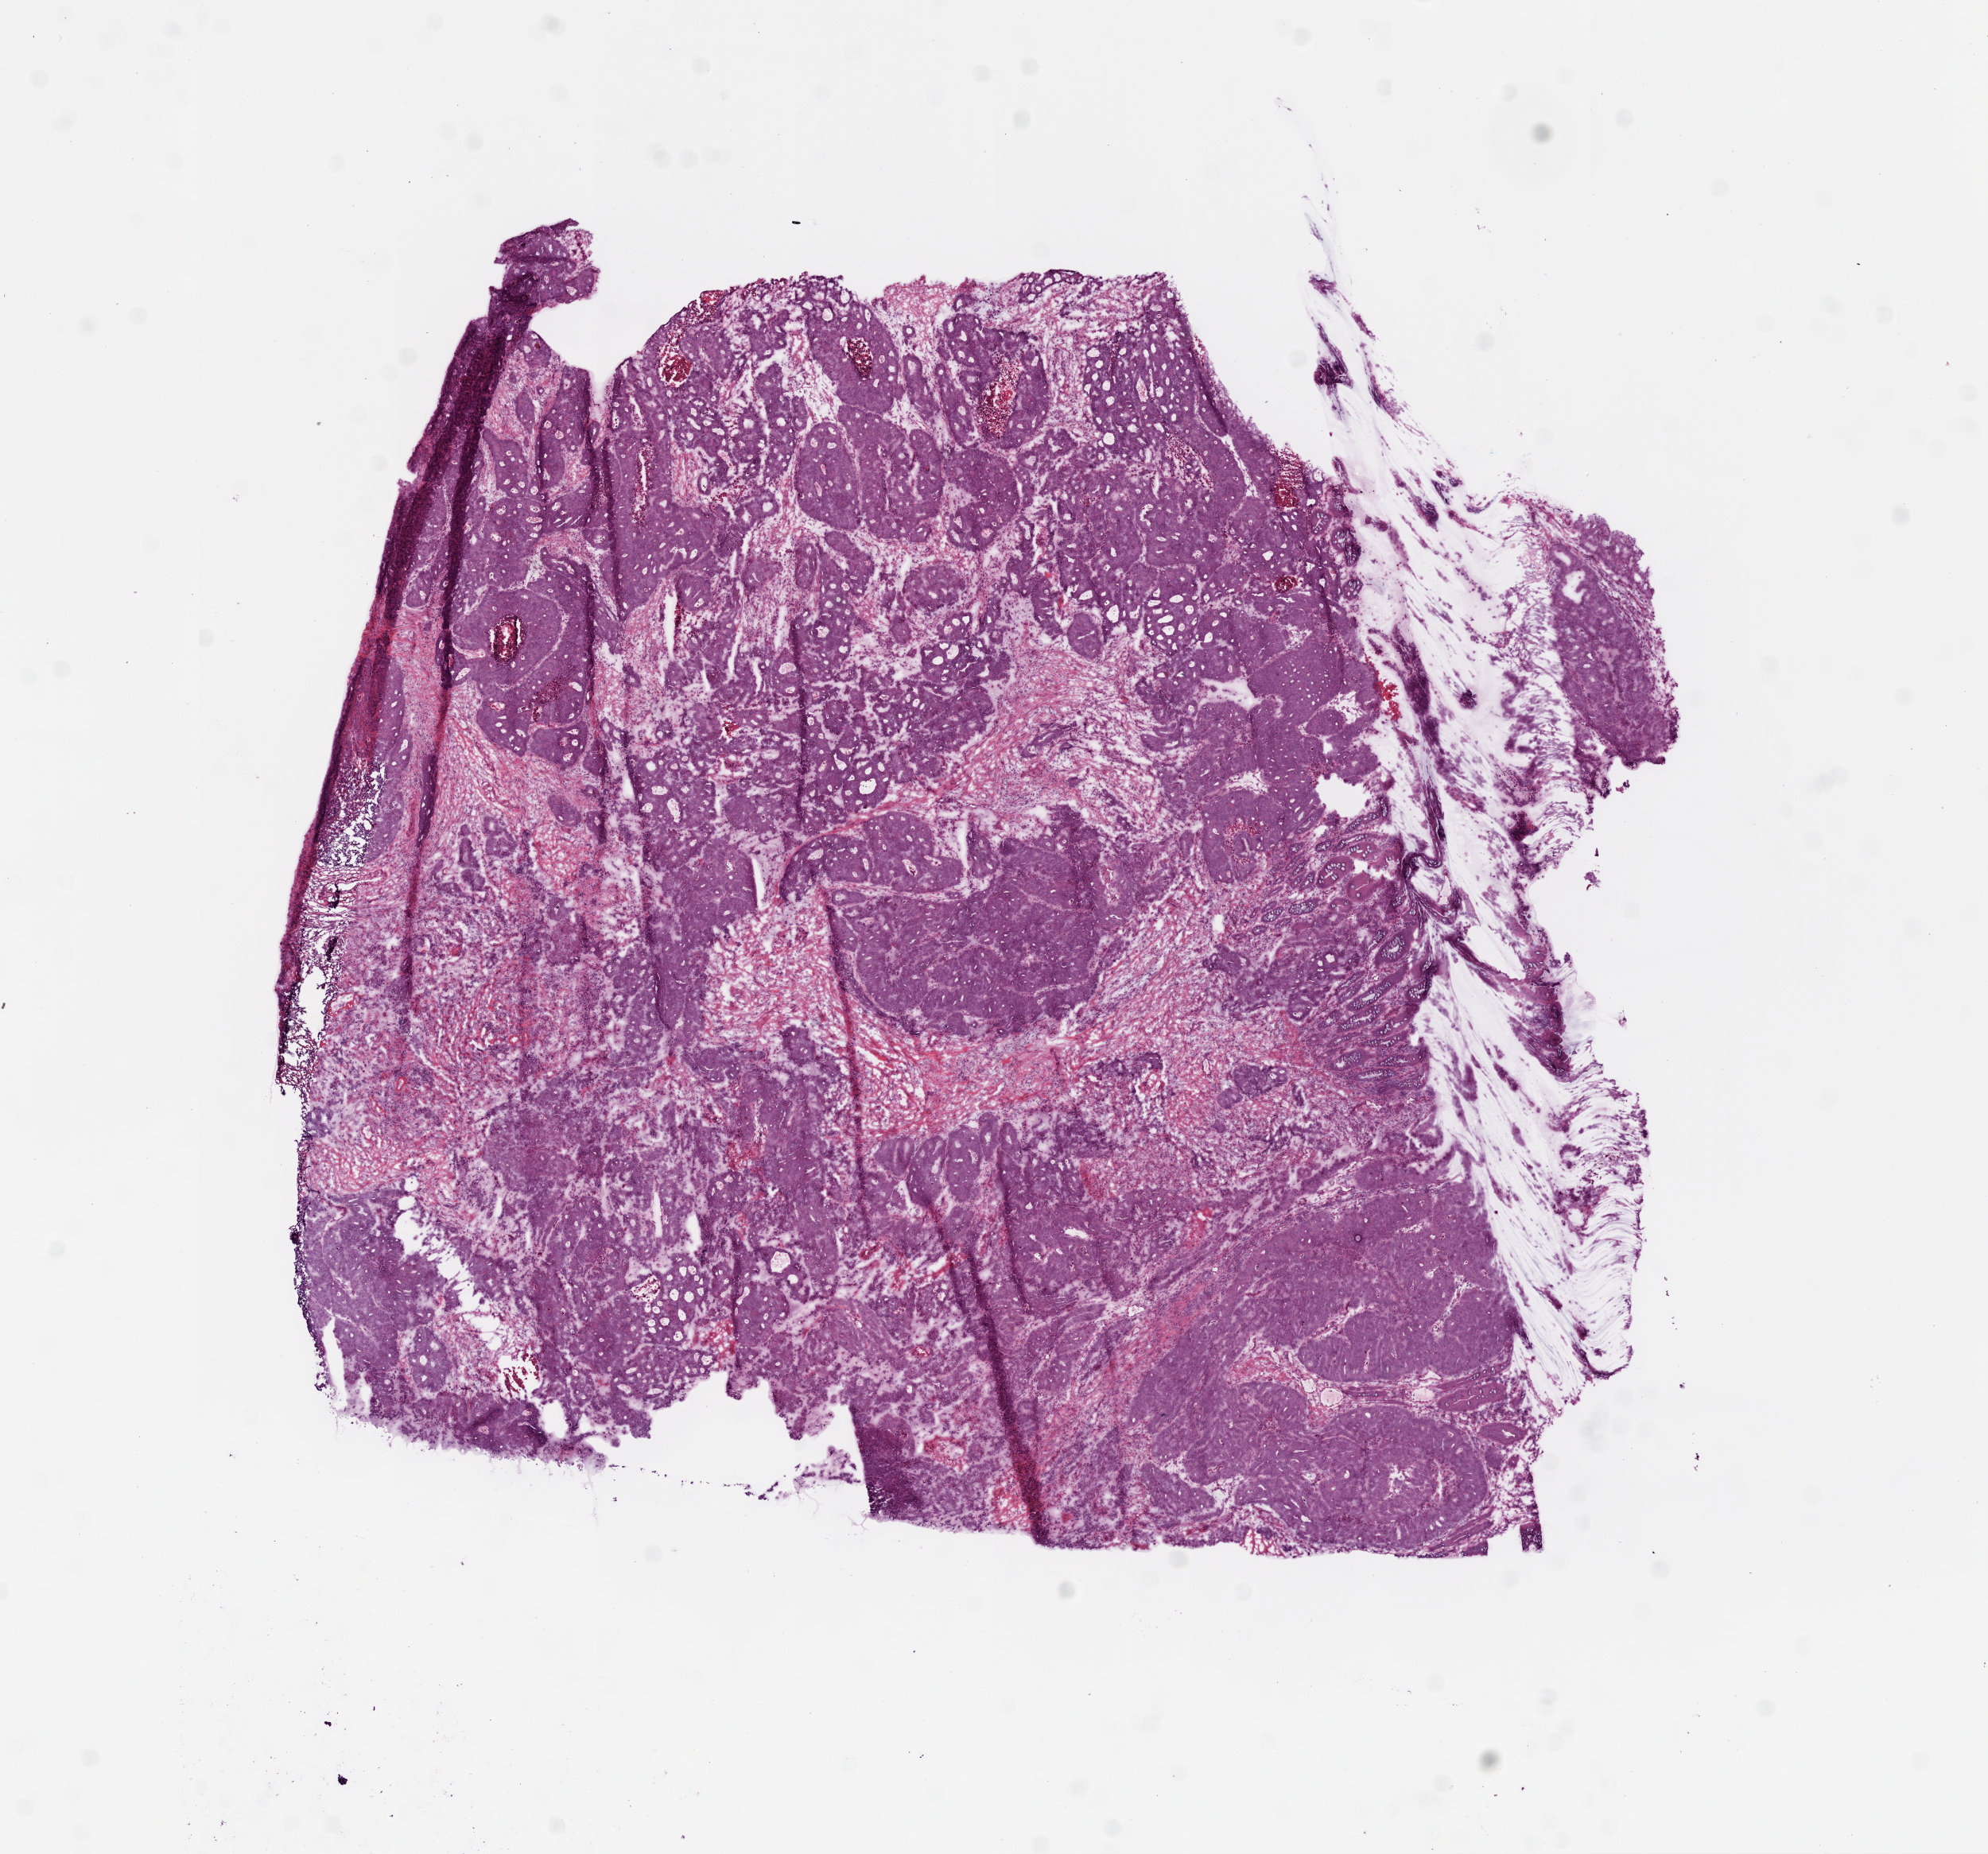
Whole-slide histology image, H&E — low-resolution overview of the scanned area, about 10.0 x 9.4 mm (from a 20x scan). Frozen section. Colon, primary tumour sample. Patient: male, age at initial diagnosis 59 years. Slide review estimates, as recorded: tumour cells 67%, tumour nuclei 75%, normal cells 3%, stromal cells 25%, necrosis 5%.
TNM: T3 N2 M1. Lymph nodes positive (case pathology): 5 of 12 examined. AJCC pathologic stage: IV (6th edition). Diagnosis: Adenocarcinoma, NOS.